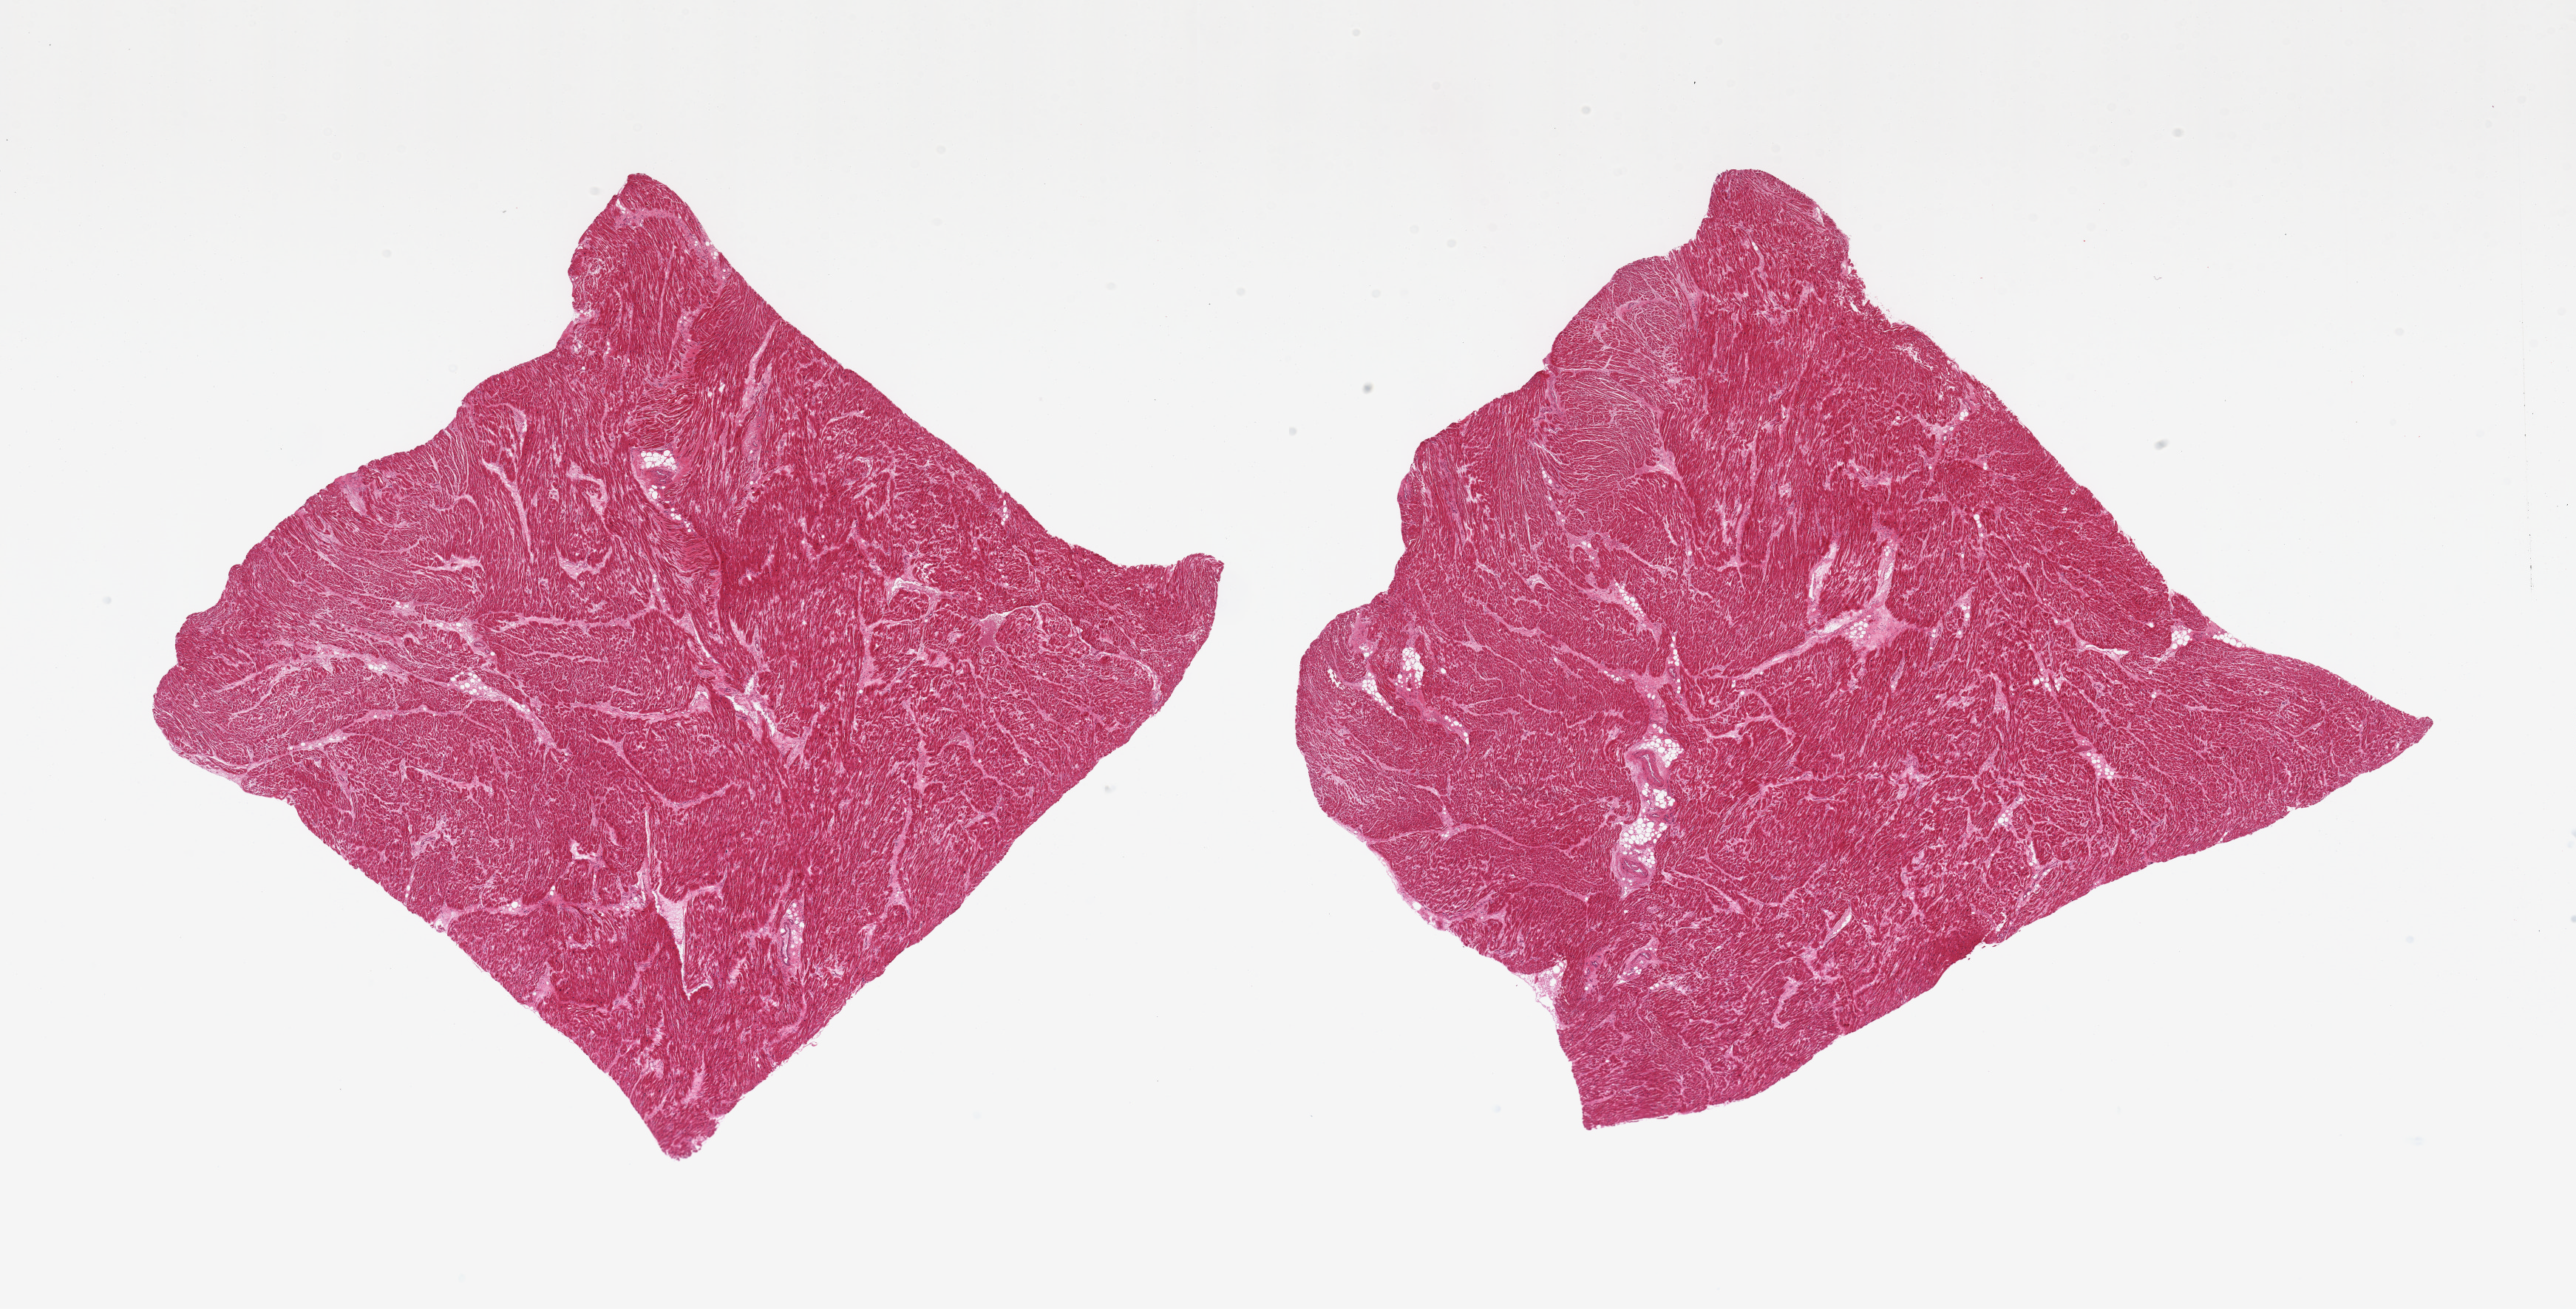
Digitized hematoxylin and eosin (H&E)-stained section, brightfield, whole scanned area (about 27.6 x 14.0 mm) shown as a low-resolution overview. PAXgene-fixed paraffin-embedded (PFPE) section. Target tissue: heart. Tissue donor sample. Donor: male.
- reviewer comment on this tissue sample: 2 pieces, moderate chronic ischemic change/interstitial fibrosis